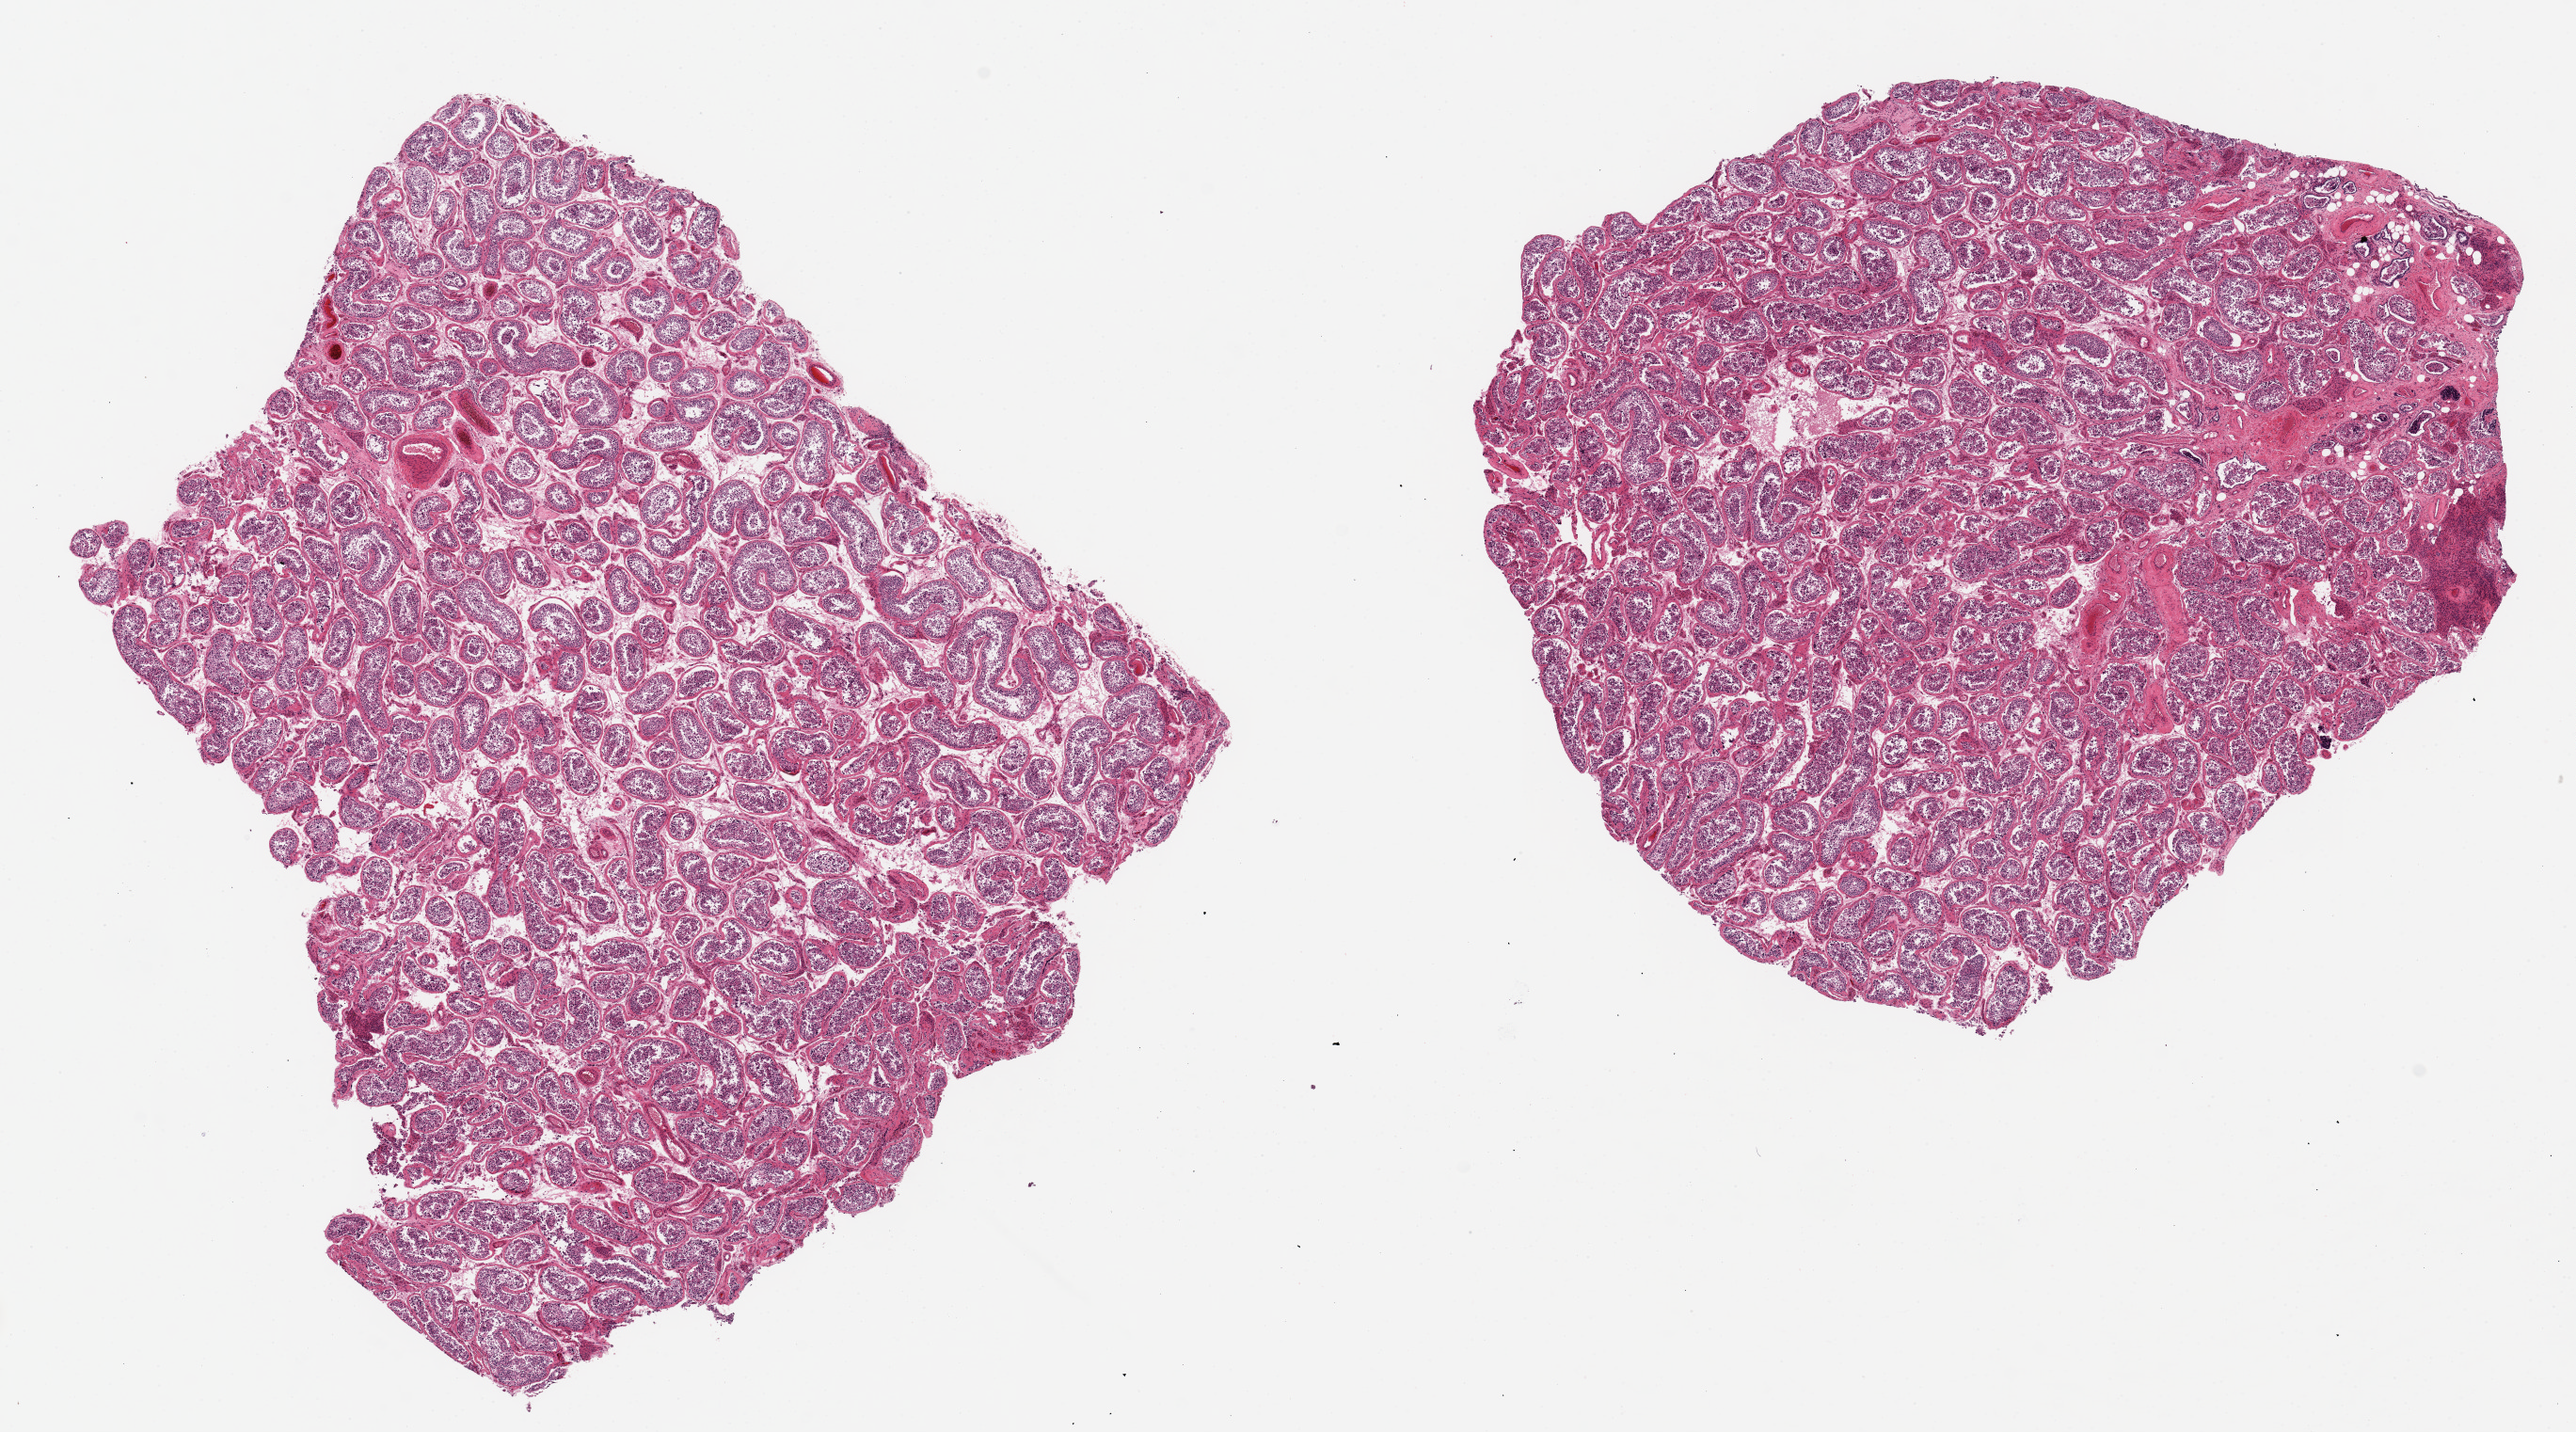
Digitized H&E-stained section, brightfield, whole scanned area (about 21.7 x 12.0 mm, acquisition: 20x scan) shown as a low-resolution overview, PAXgene-fixed, paraffin-embedded tissue, sampled site (target tissue): testis, donor tissue sample. Donor: male.
Reviewer comment on this tissue sample: 2 ~8.5x7.5mm aliquots. Leydig cells seem unusually prominent. Spermatogenesis assessment hampered by unusually poor preservation.